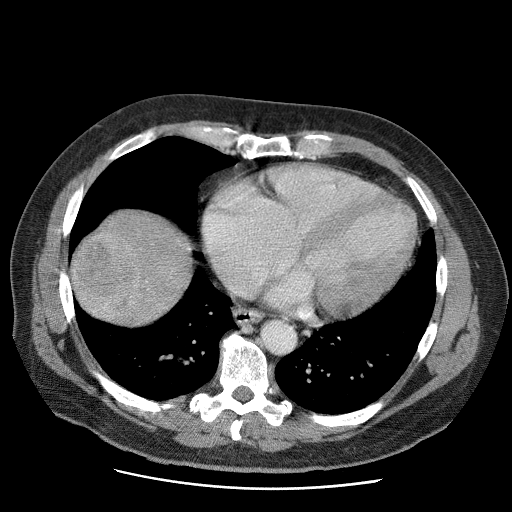
Contrast-enhanced abdominal CT (liver protocol), one axial slice. Slice 63 of 81 in the series (ordered by position). Reconstruction kernel STANDARD. Soft-tissue window (W 400 / L 40 HU). 512 × 512 image matrix, field of view 380 × 380 mm. From the clinical record (not read from this slice): diagnosis: hepatocellular carcinoma (patient treated with transarterial chemoembolisation; whether this scan precedes or follows treatment is not stated here); TNM stage (as recorded): Stage-IIIA; Child-Pugh class: A.
Outlined on this slice (semi-automatically segmented with operator editing):
- liver parenchyma outside the tumour (the mass and vessels are separate outlines, so this box may not span the whole liver): bounding box (x1, y1, x2, y2) in pixels: (70, 208, 190, 322)
- mass: (72, 232, 141, 321)